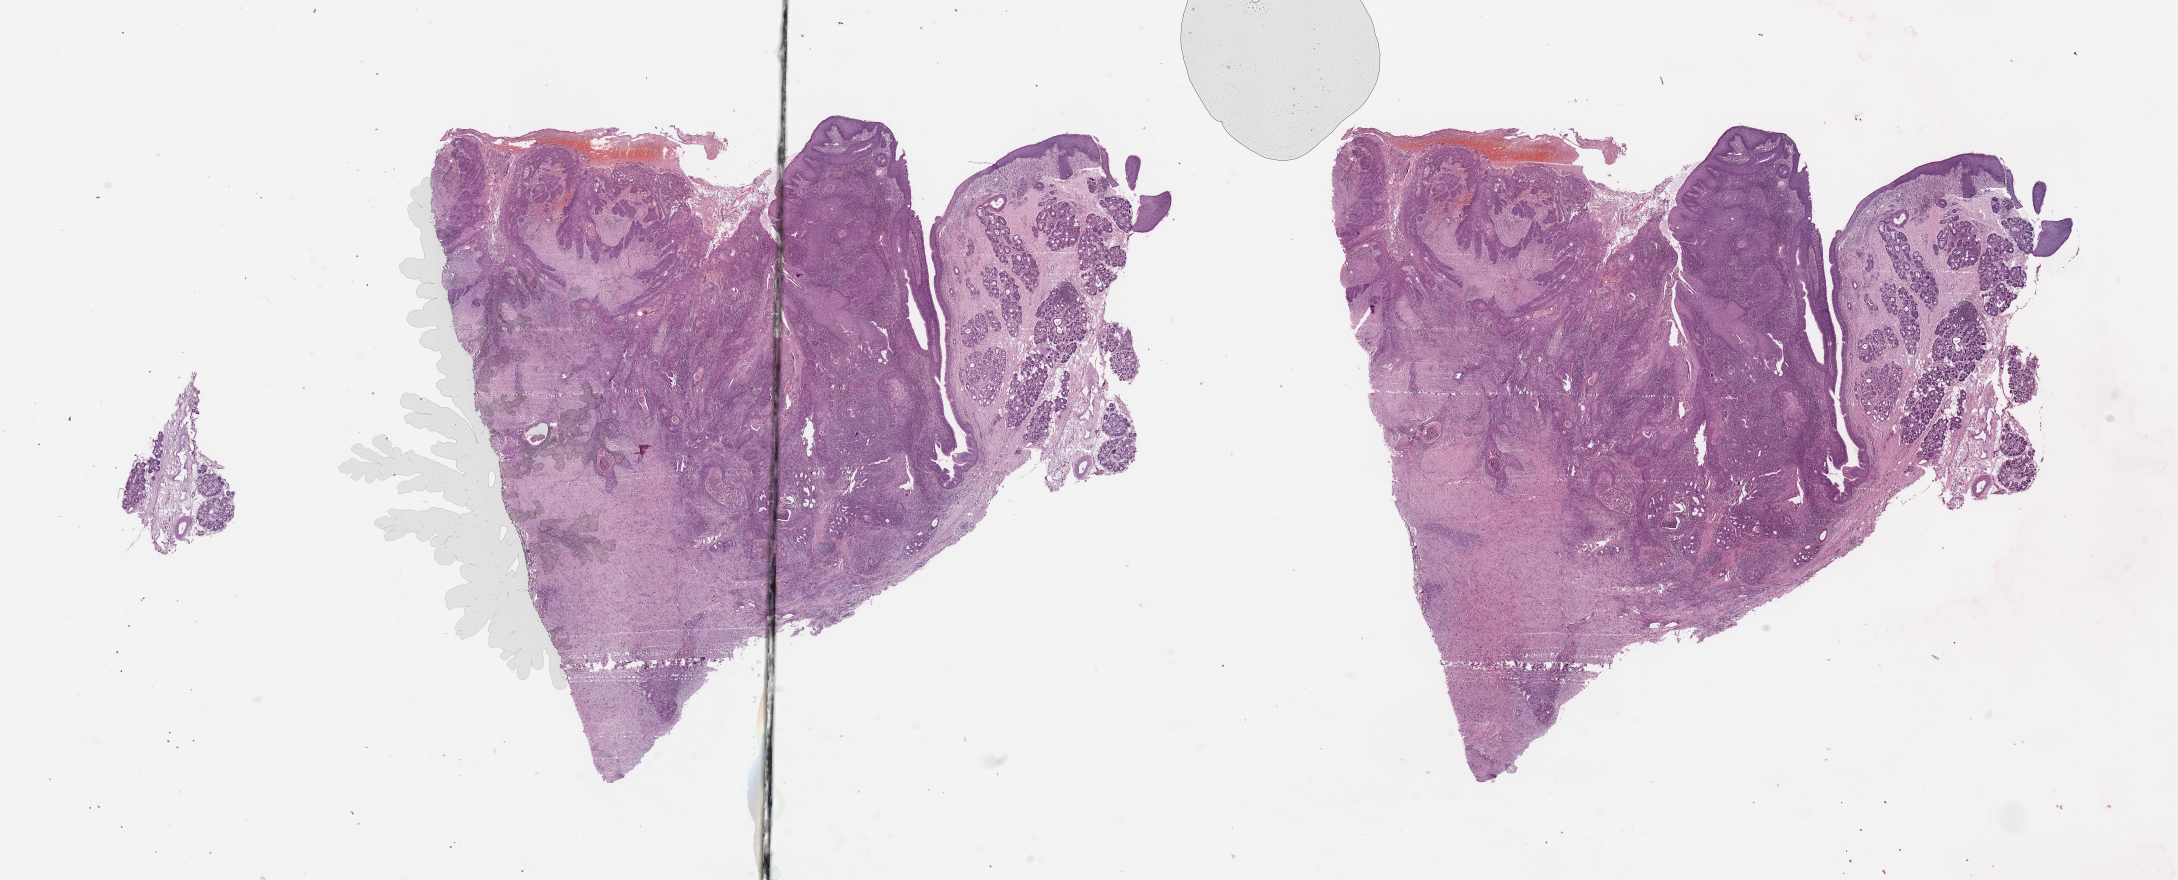
Whole-slide histology image, H&E-stained — low-resolution overview of the scanned area, about 34.5 x 13.9 mm (slide scanned at 20x); tumour tissue sample, sampled site: larynx. Patient: male, age 49 years. Histologic grade: G2 (moderately differentiated). Composition of this section per pathologist review: tumour nuclei 70%, necrosis 5%.
Histologic diagnosis: Squamous cell carcinoma, NOS (larynx, NOS). AJCC pathologic stage: IVA.